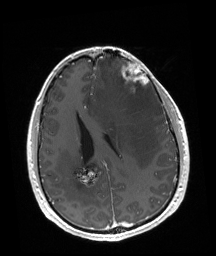
Brain MRI from a brain-tumour surgery series, one axial slice. Slice 71 of 192 in the series (ordered by position). T1-weighted post-contrast. 1 mm slice thickness. 216 × 256 image matrix, field of view 219 × 260 mm. Case-level facts recorded for this patient, not image findings: tumour location: Left Frontal.
Outlined on this slice (manually delineated by an expert):
- tumour: bounding box (x1, y1, x2, y2) in pixels: (121, 64, 149, 93)